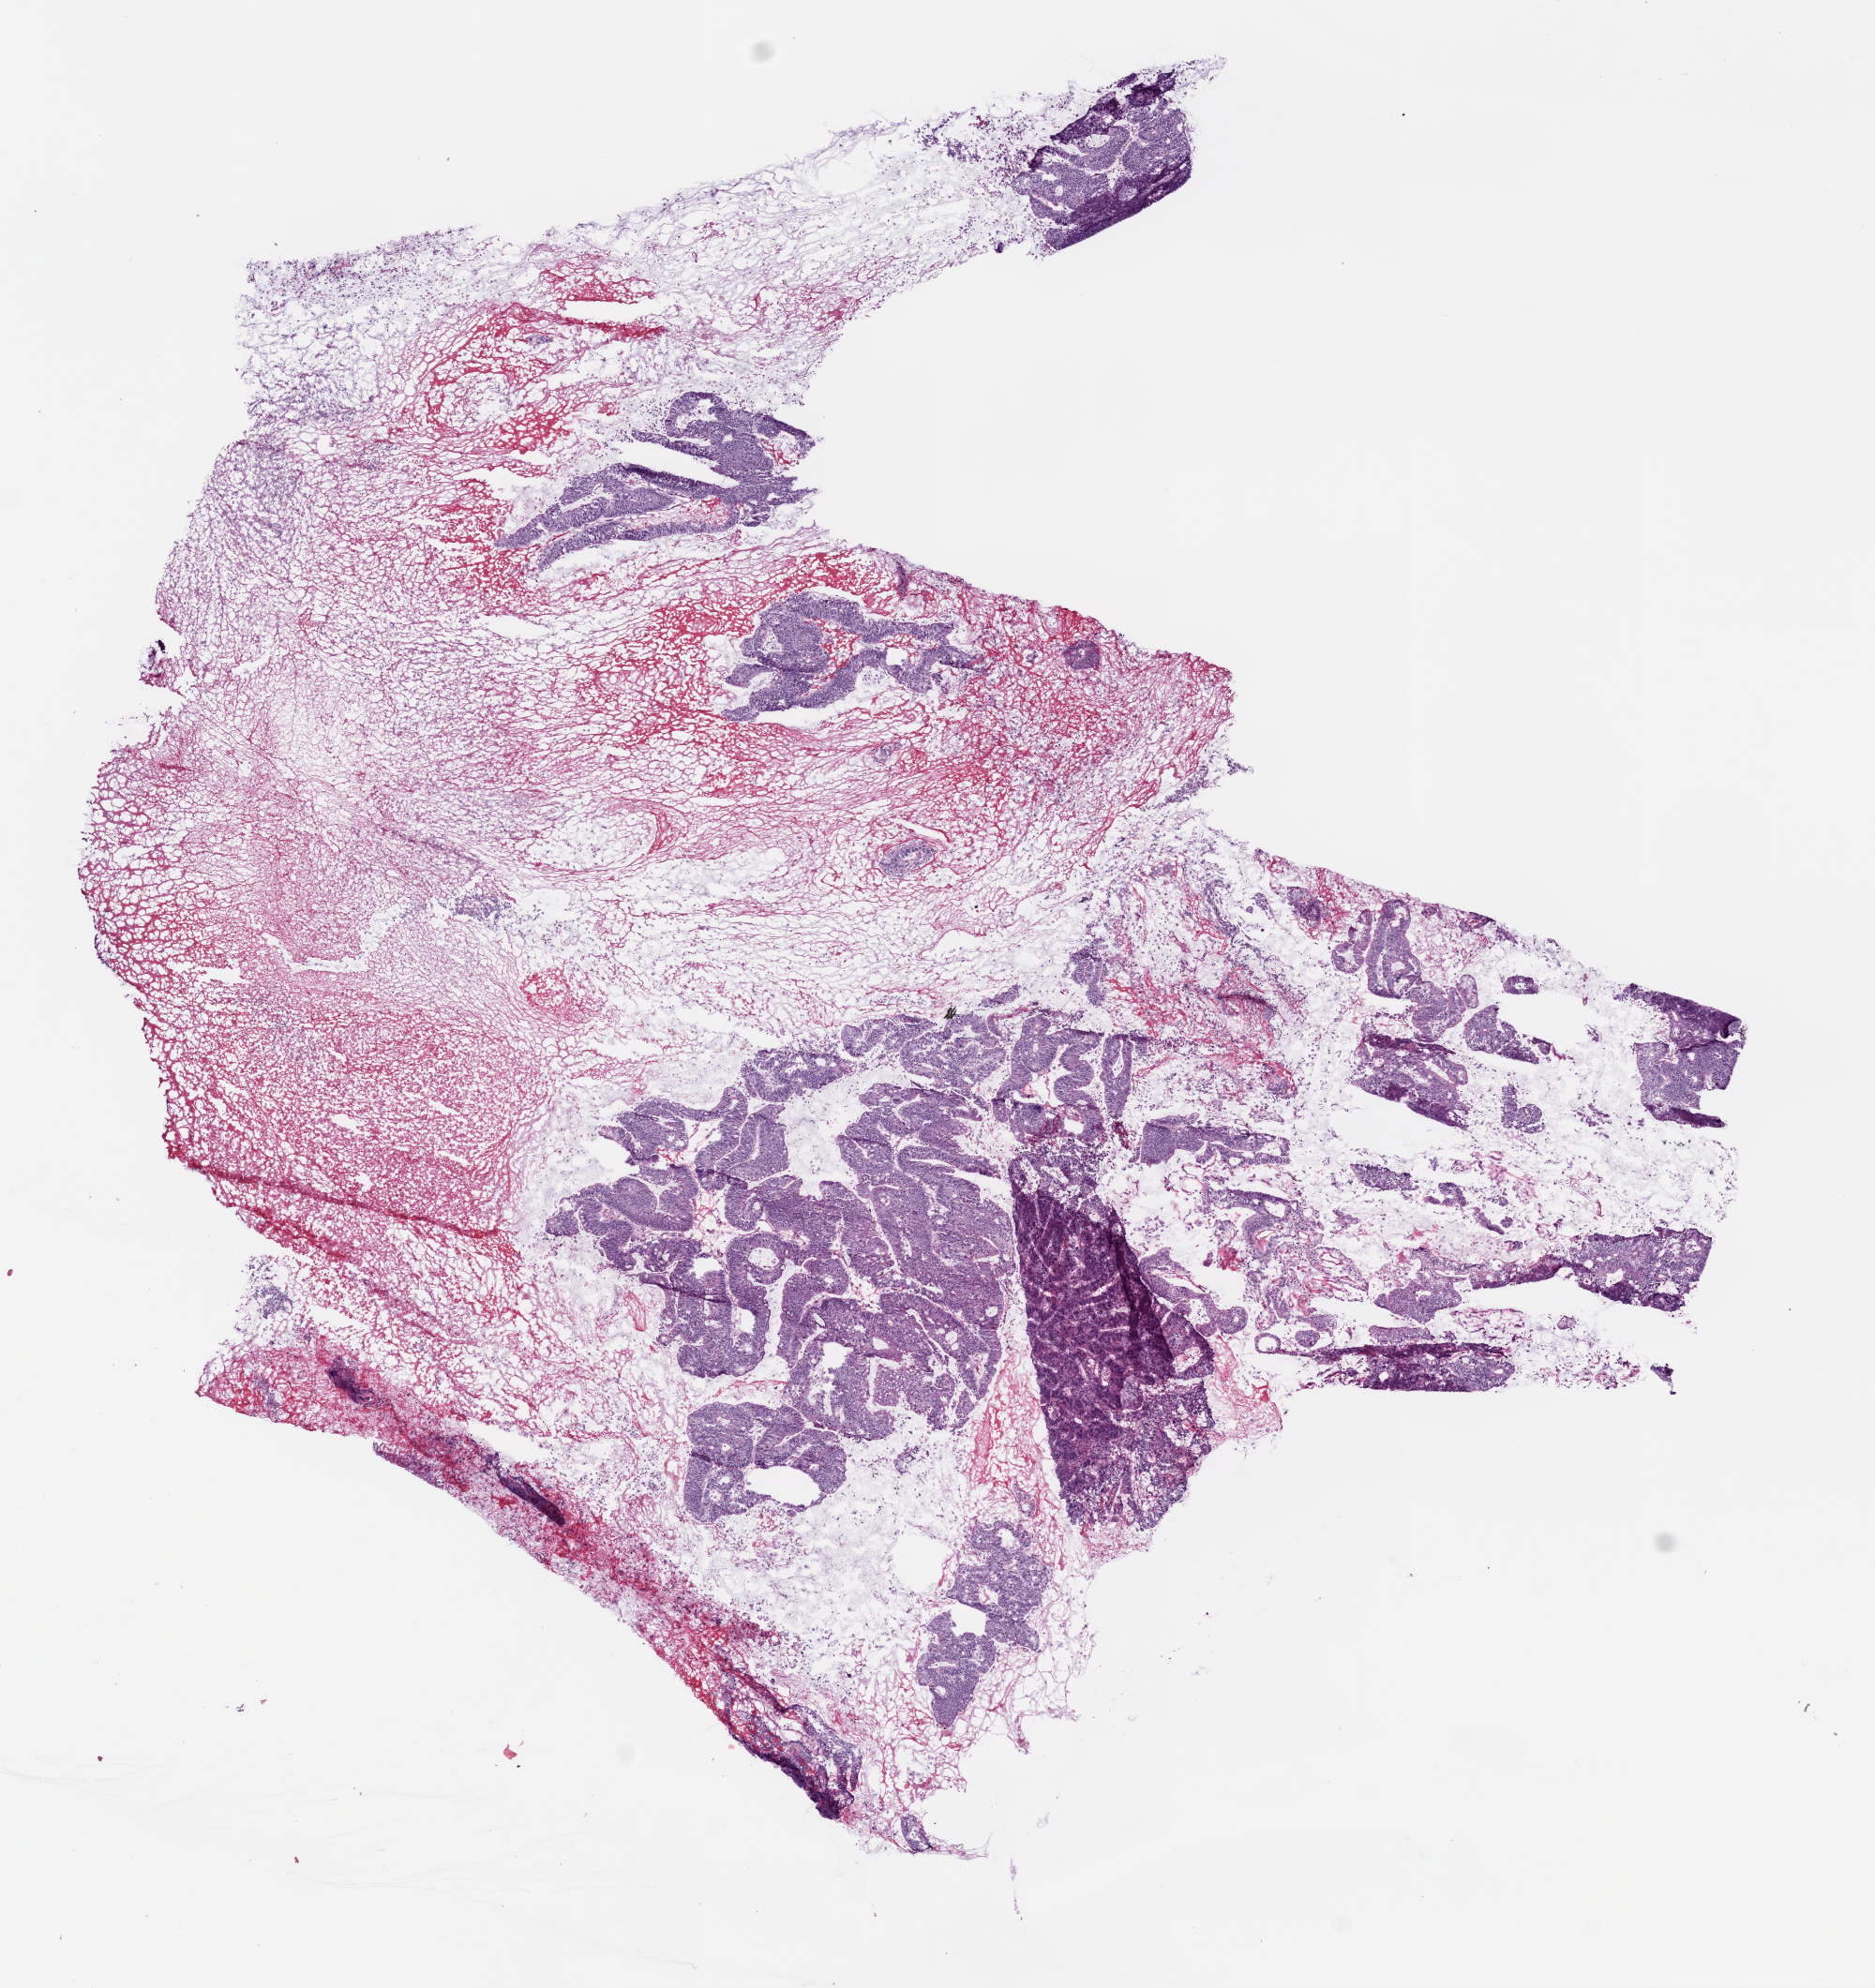
Whole-slide histology image, H&E, whole scanned area (about 8.0 x 8.5 mm, acquisition: 20x scan) shown as a low-resolution overview, frozen section, sample: primary tumour, colon. Patient: male, age at initial diagnosis 70 years. Composition of this section per pathologist review: tumour cells 40%, tumour nuclei 80%, normal cells 0%, stromal cells 60%, necrosis 0%.
* TNM: T2 N0 M0
* pathologic diagnosis: Adenocarcinoma, NOS (sigmoid colon)
* AJCC pathologic stage: I (6th edition)